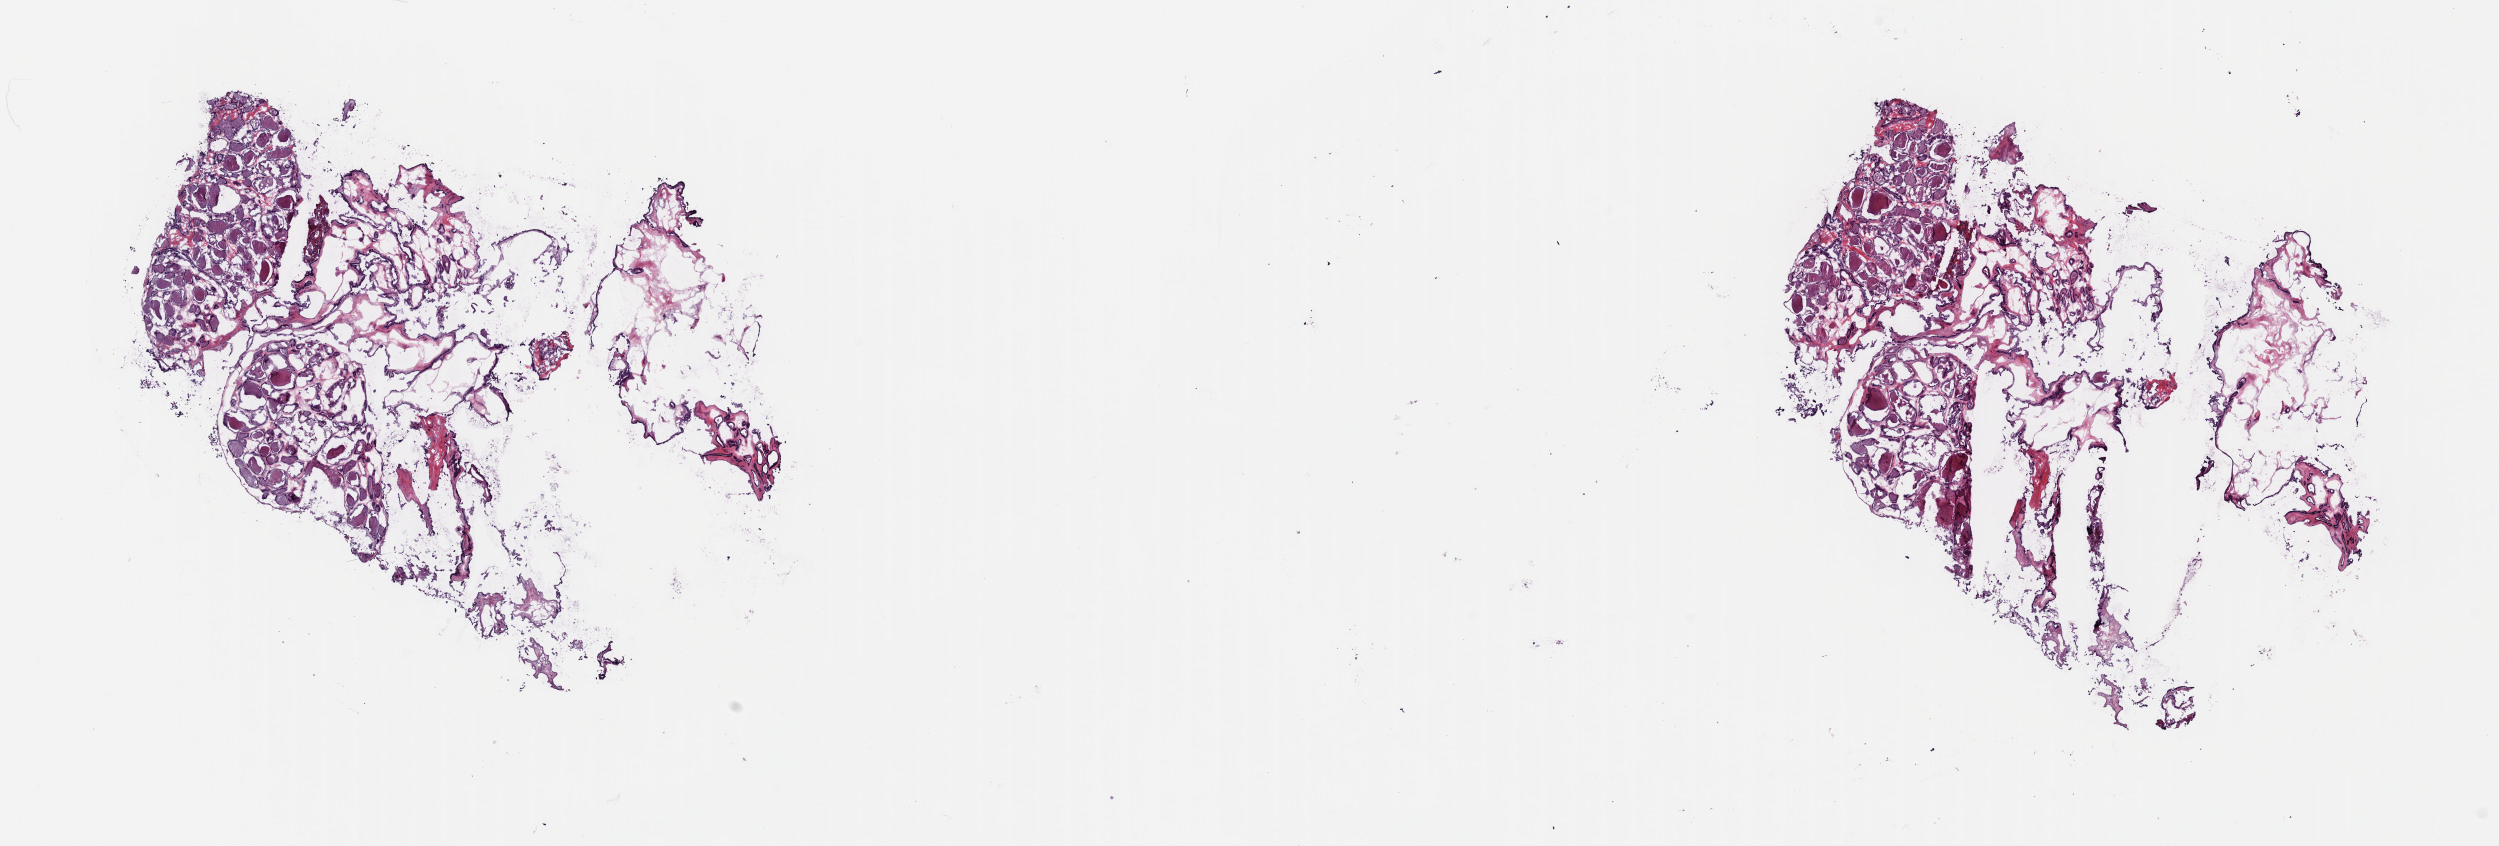
H&E-stained whole-slide image, whole scanned area (about 19.7 x 6.7 mm) shown as a low-resolution overview; frozen section; thyroid, primary tumour sample. Female, age 70 years at initial diagnosis. Composition of this section per pathologist review: tumour cells 100%, tumour nuclei 90%, normal cells 0%, stromal cells 0%, necrosis 0%. Inflammatory infiltration, as recorded: lymphocyte infiltration 0%, monocyte infiltration 0%, neutrophil infiltration 0%.
AJCC pathologic stage: II (4th edition). Pathologic diagnosis: Papillary adenocarcinoma, NOS (thyroid gland).